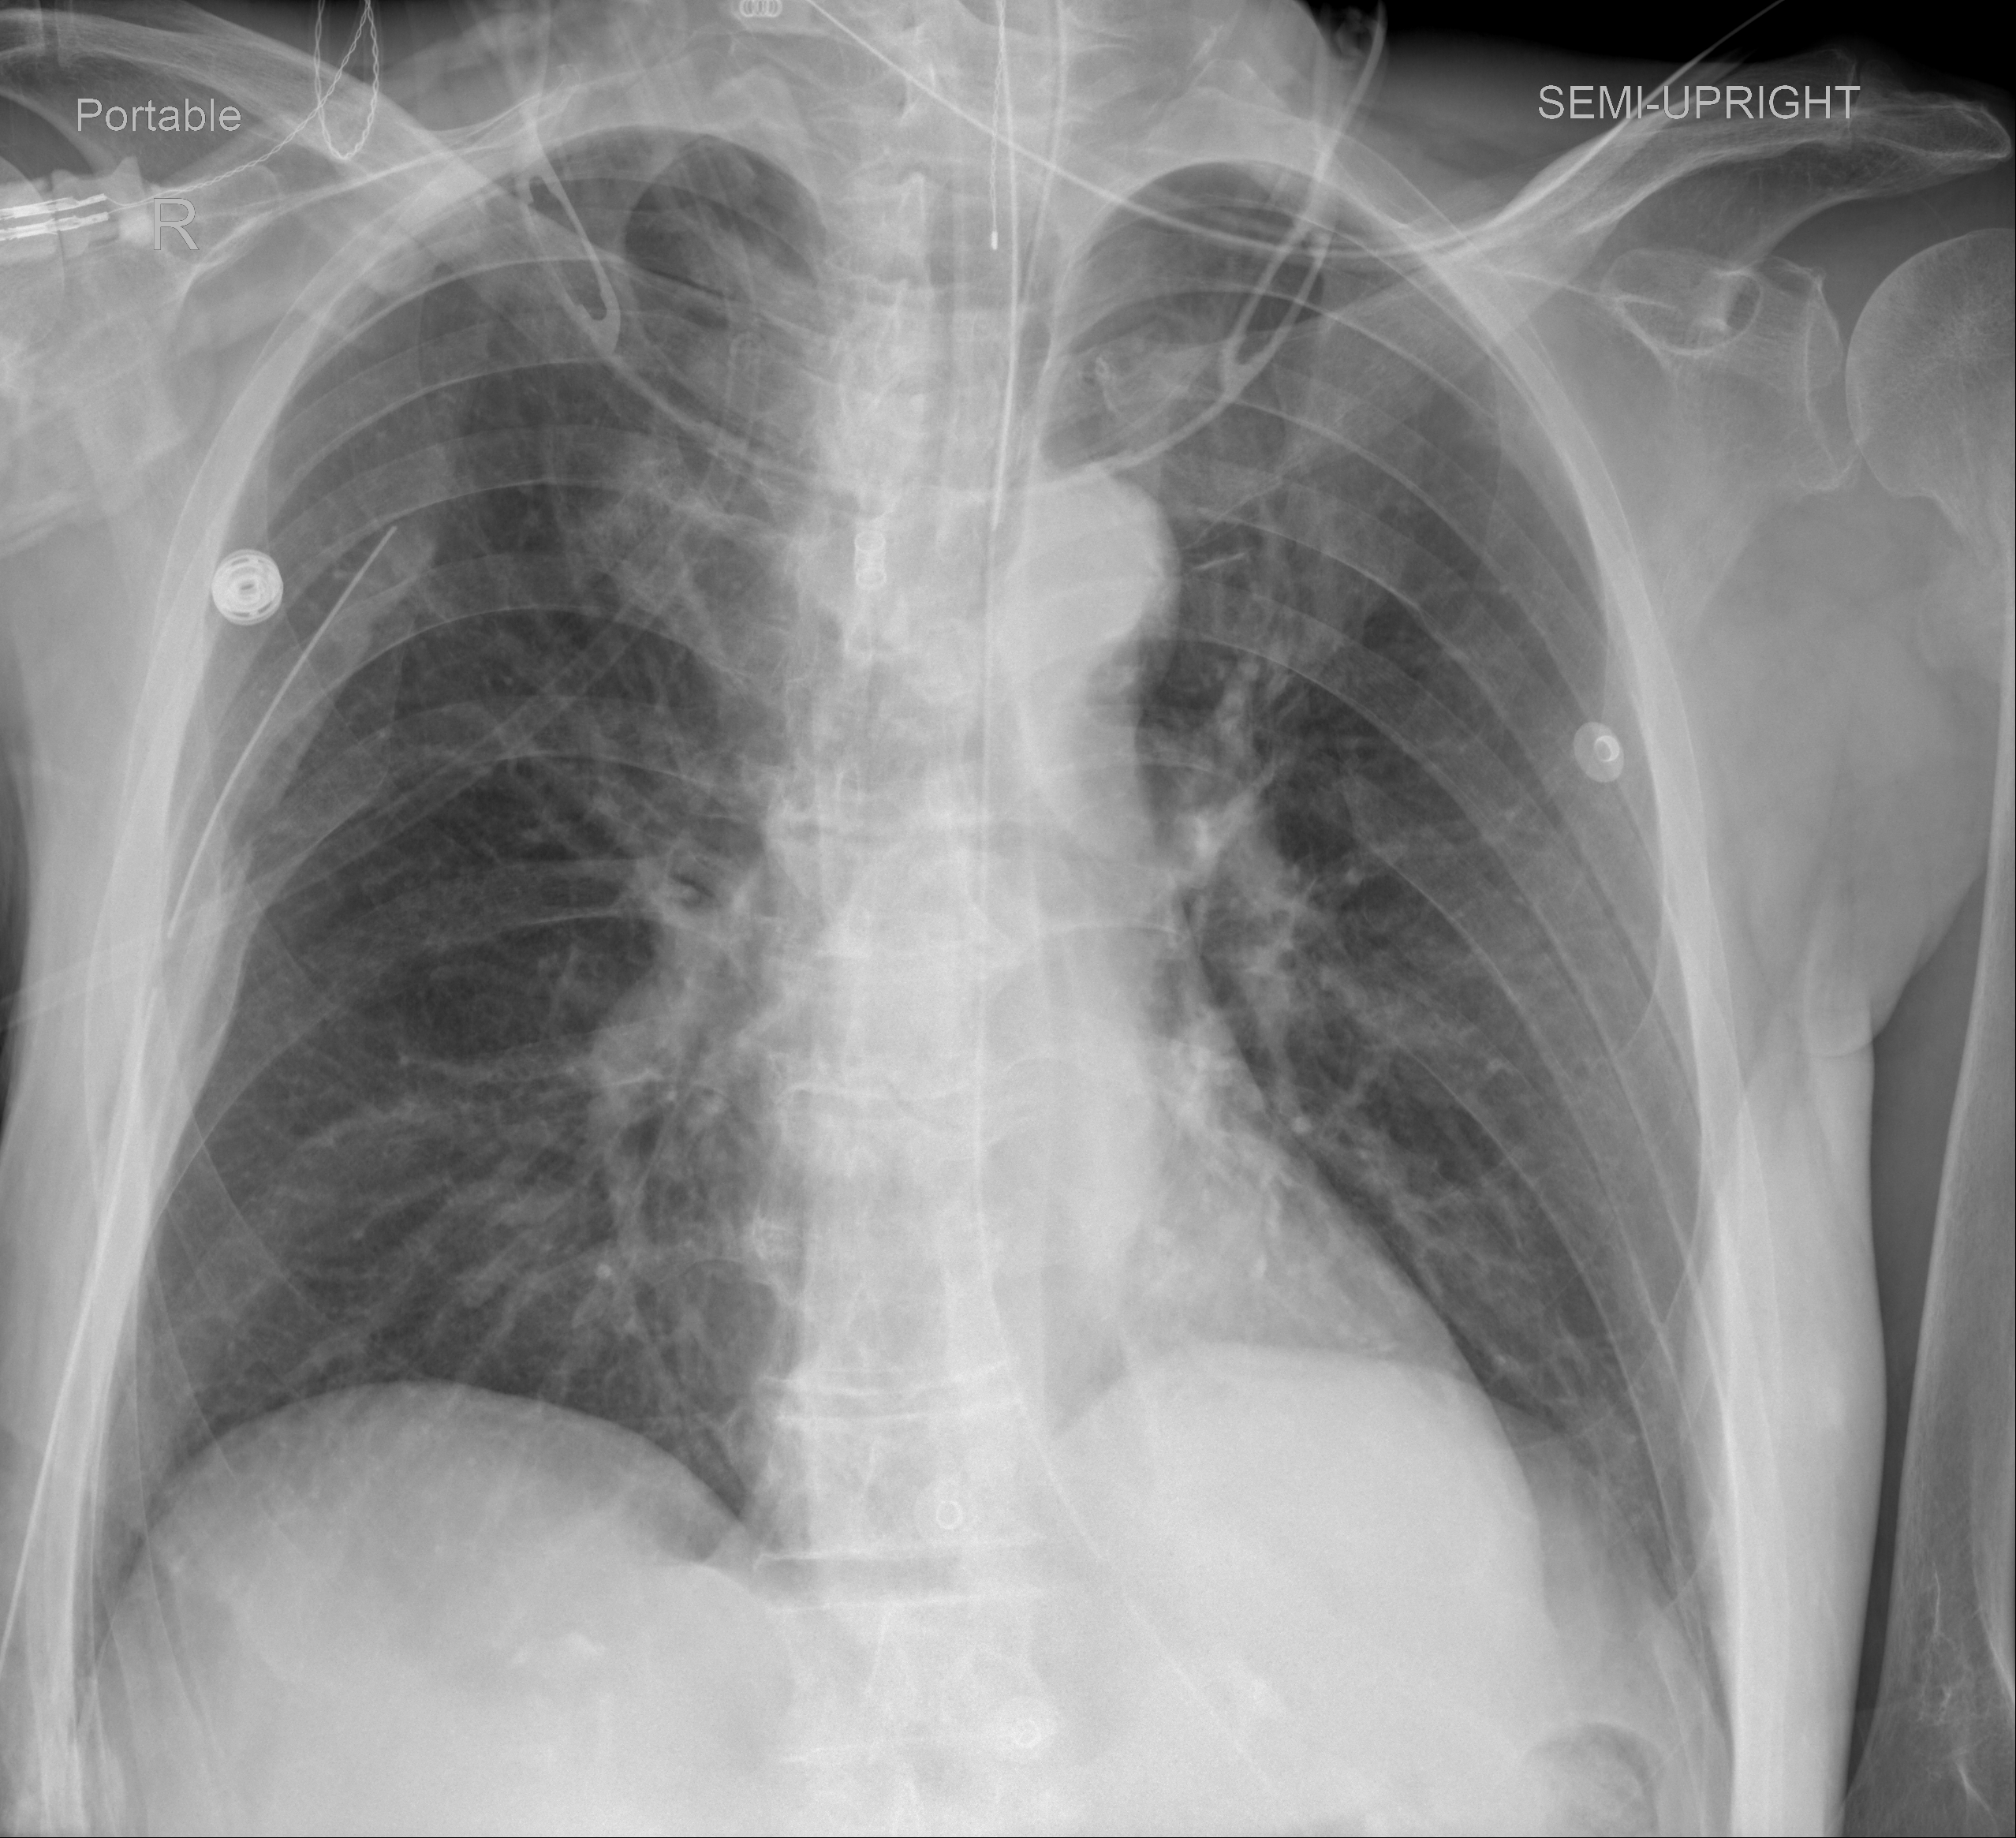
Chest X-ray (portable), AP projection. Male patient, age 59 years; imaged 1 day after the COVID-19 diagnosis.
Radiologist key findings (as recorded): The lungs remain clear. No pleural effusion.